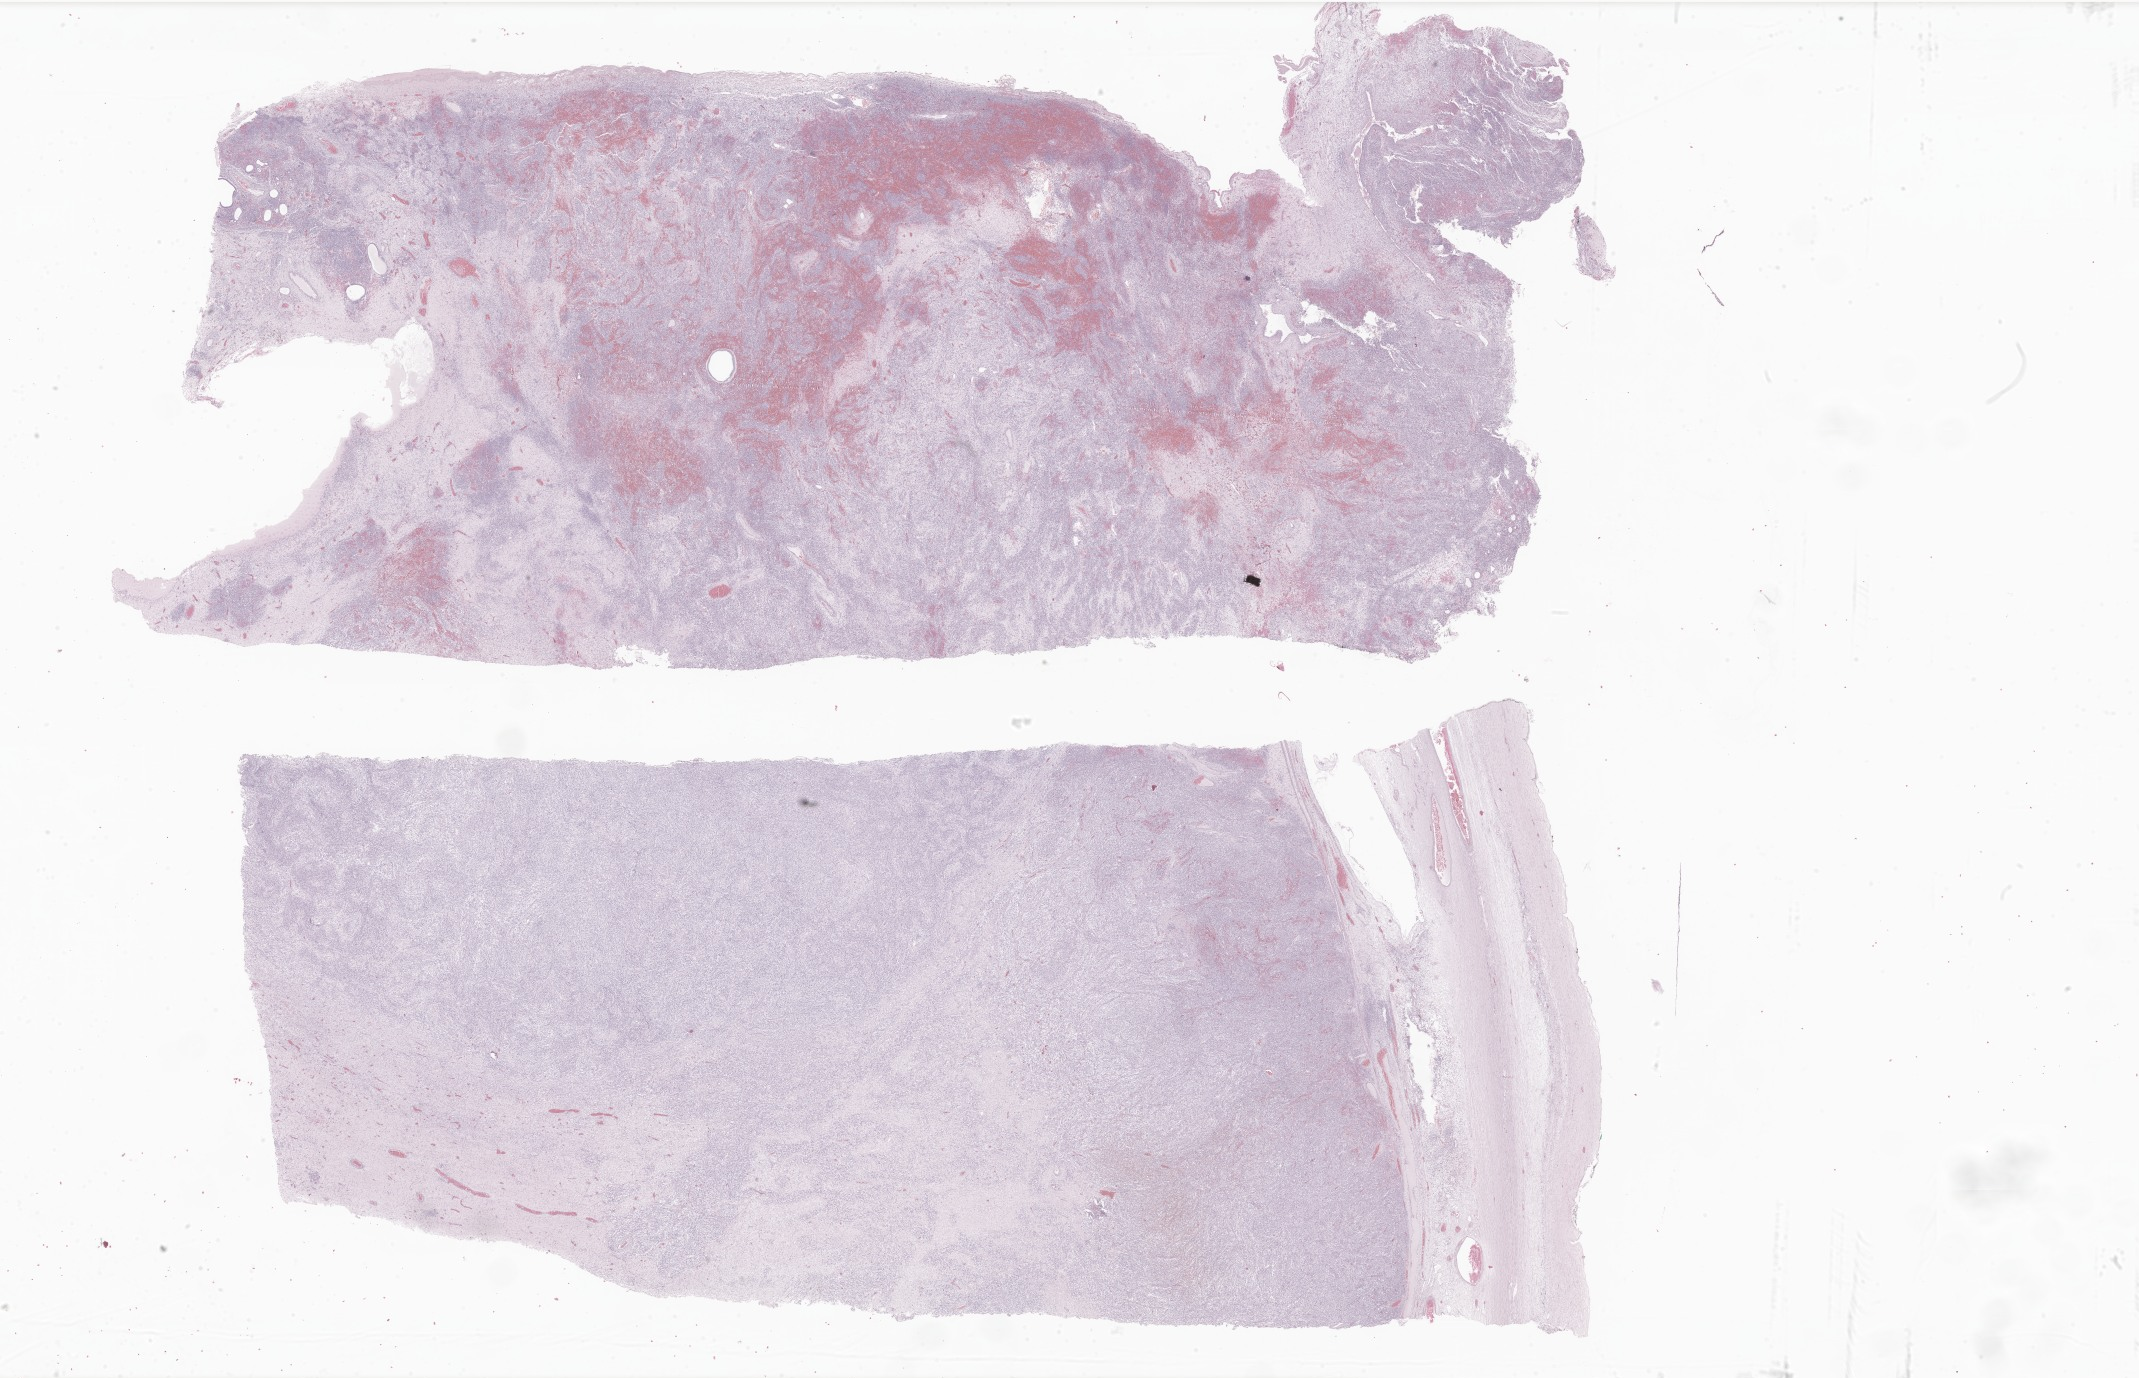
Whole-slide image, haematoxylin and eosin stain of tumor tissue from the ovary, shown as a low-resolution overview of the whole scanned area (about 36.1 x 23.2 mm), formalin-fixed, paraffin-embedded (FFPE) tissue. Patient: female, age 223 months (18 years 7 months).
• diagnosis: Embryonal rhabdomyosarcoma, NOS